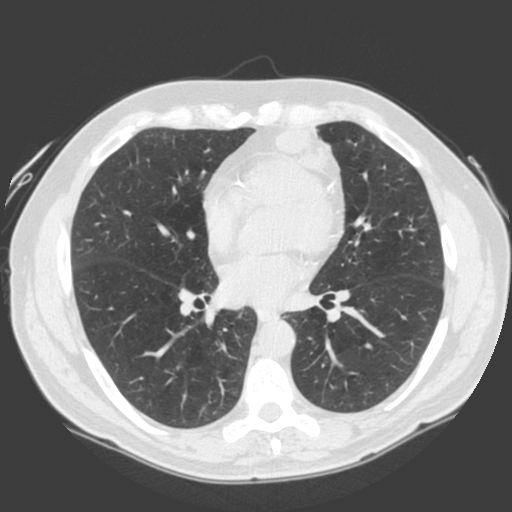
Low-dose screening chest CT, one axial slice; slice 89 of 185 in the series (ordered by position); 120 kVp; lung window (W 1500 / L -600 HU); 2 mm slice thickness; 512 × 512 image matrix, field of view 360 × 360 mm.
Annotated regions visible in this slice (expert manual segmentation):
- lesion 1 (tumor, lower lobe of left lung): bounding box <275,125,339,177> (left, top, right, bottom; pixels)